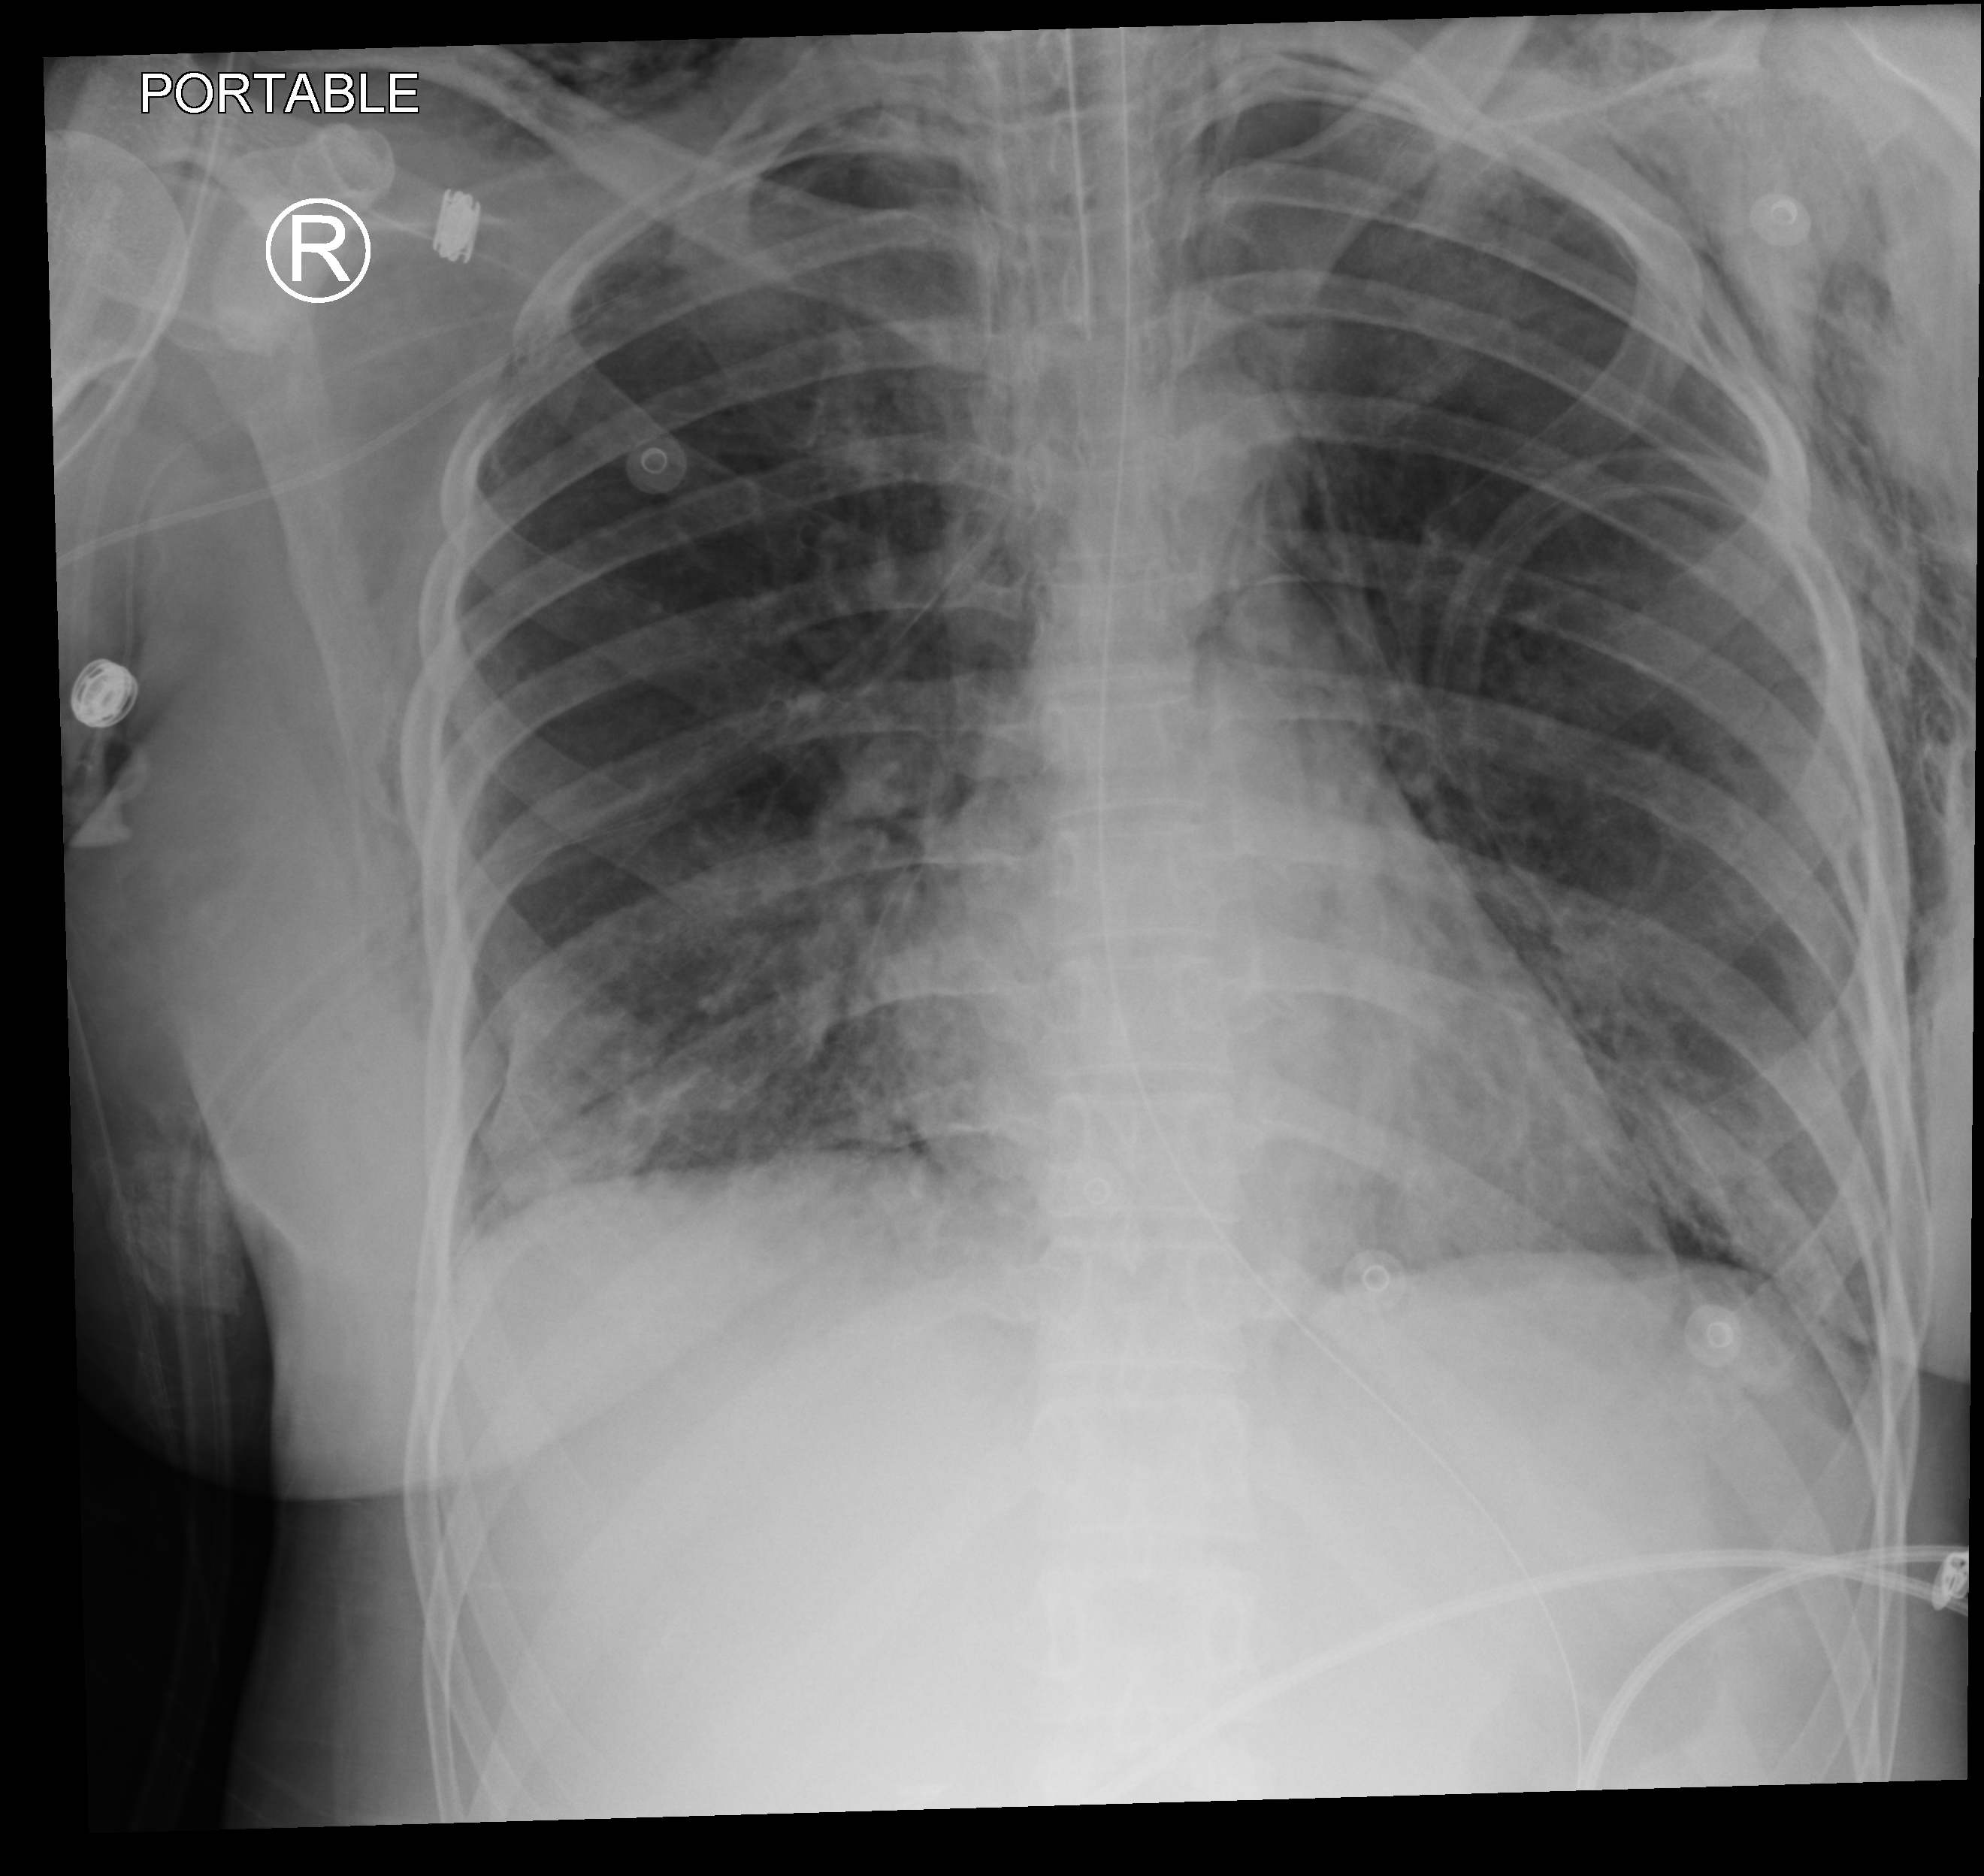
Bedside chest radiograph (computed radiography). Patient hospitalised with COVID-19, aged 18–59 years.
From the hospital-stay record, not from the radiograph (when in the stay this image was taken is not recorded): hypertension (admission record): no.